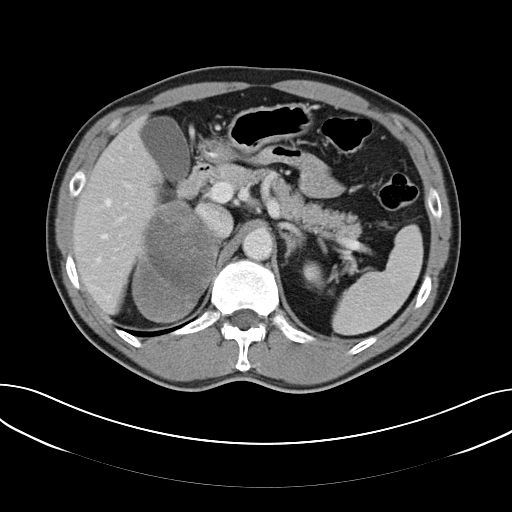
Contrast-enhanced abdominal CT, one axial slice. Position 37 of 61 along the scan axis. Reconstruction kernel B40f. Intravenous contrast given. Soft-tissue window (W 400 / L 40 HU). 5 mm slice thickness. 512 × 512 image matrix, field of view 372 × 372 mm. Patient: male, 57 years. From the clinical record (not read from this slice): diagnosis: adrenocortical carcinoma; tumour side: right adrenal; tumour size at pathology: 11.2 cm.
Structures marked on this image (semi-automatic segmentation, software-assisted and operator-edited):
- mass: box from (x=133, y=203) to (x=216, y=323) px